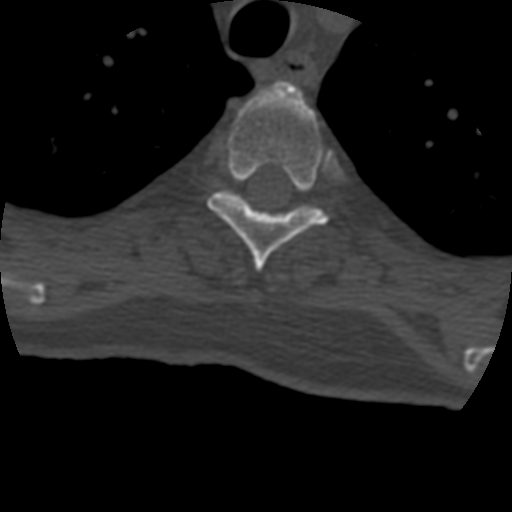
CT including the spine, one axial slice. Position 336 of 399 along the scan axis. 120 kVp. Bone window (W 1800 / L 400 HU). 512 × 512 image matrix. Patient age 69 years. From the clinical record (not read from this slice): primary cancer: prostate.
Outlined on this slice (semi-automatically segmented with operator editing):
- T4 vertebra: bounding box [x1, y1, x2, y2] px = [207, 88, 329, 272]